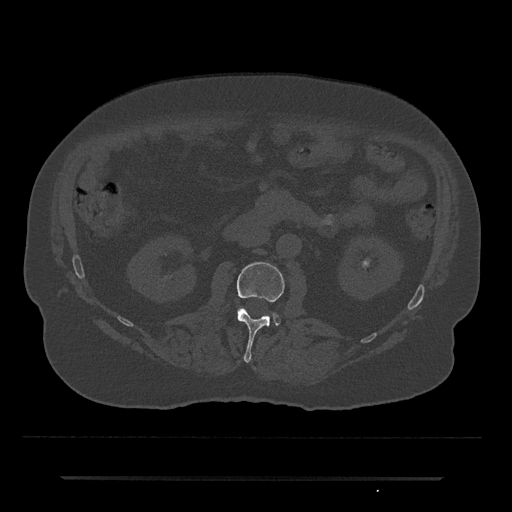
CT including the spine, one axial slice. Position 1 of 797 along the scan axis. Reconstruction kernel Br40s/3. 120 kVp. Bone window (W 1800 / L 400 HU). 0.5 mm slice thickness. 512 × 512 image matrix, field of view 437 × 437 mm. Male patient, age 69 years. Case-level facts recorded for this patient, not image findings: primary cancer: prostate.
Structures marked on this image (semi-automatically segmented with operator editing):
- L2 vertebra: bounding box [x1, y1, x2, y2] px = [237, 262, 284, 362]